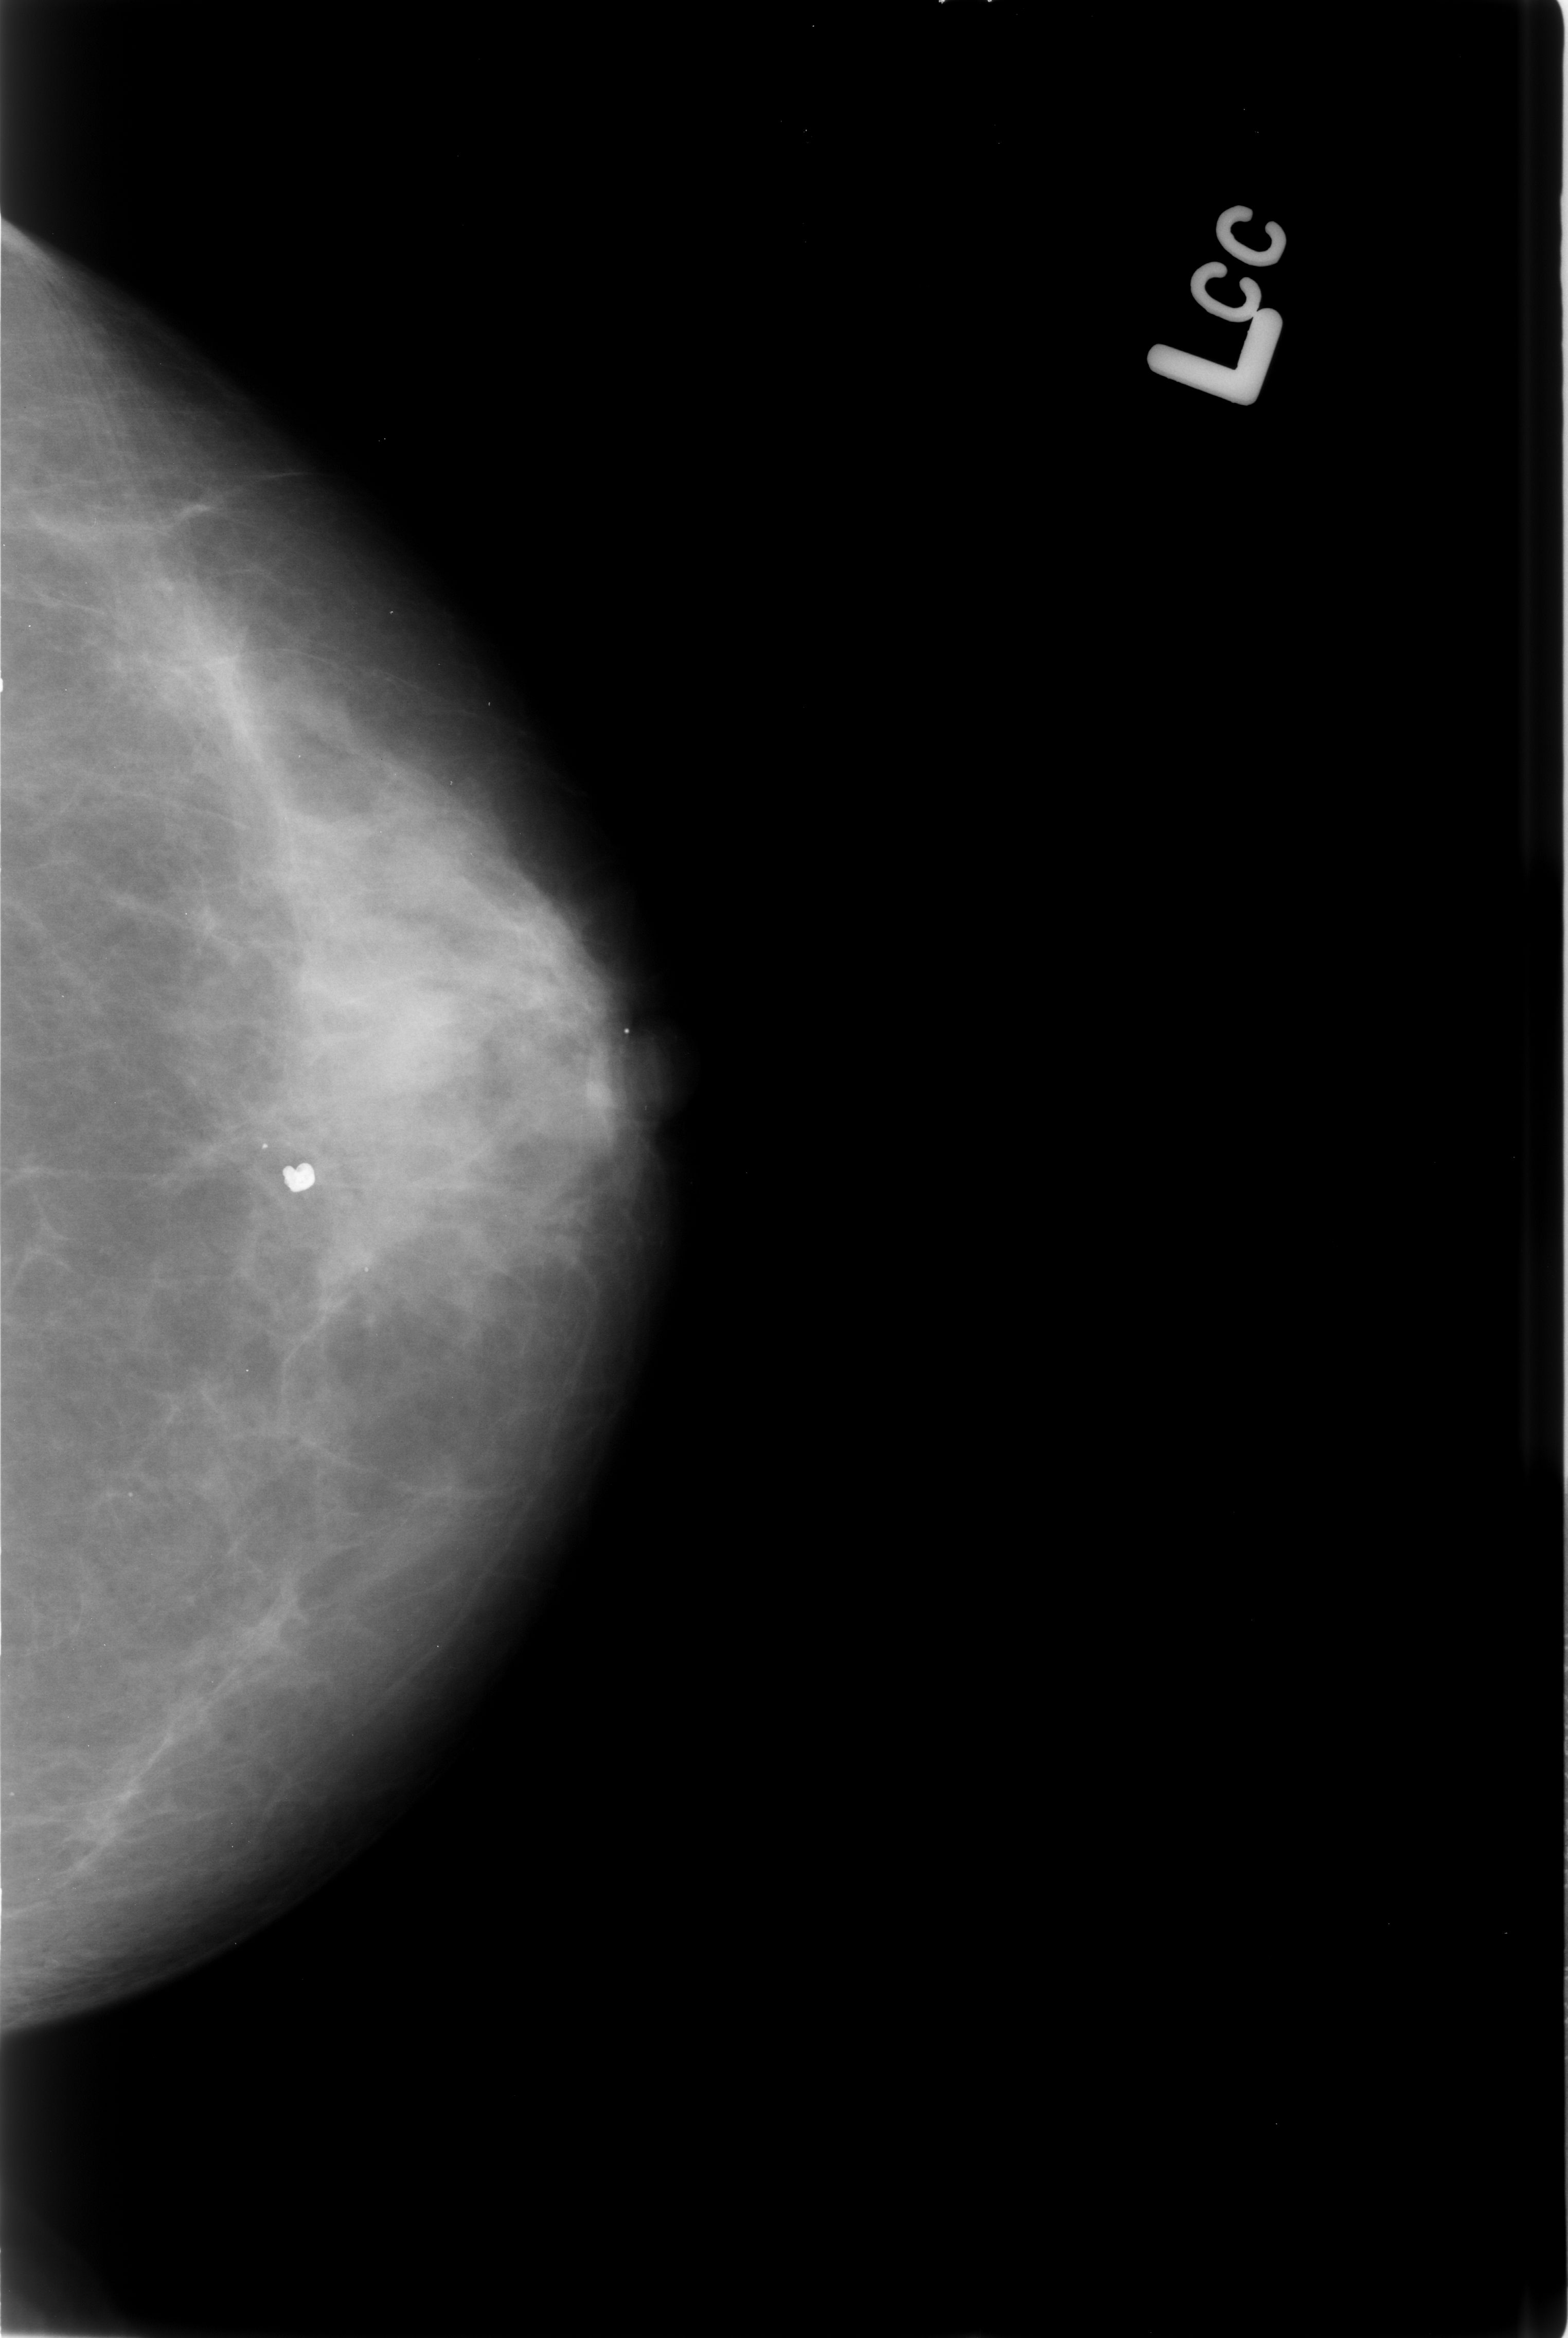
Digitized screen-film mammogram; left breast; CC view.
Marked findings (only marked abnormalities are described; nothing is implied about the rest of the image): calcifications, morphology coarse; BI-RADS assessment category 2; subtlety rating 5 on a 1 (subtle) to 5 (obvious) scale; benign; no additional work-up was recommended (benign without callback).